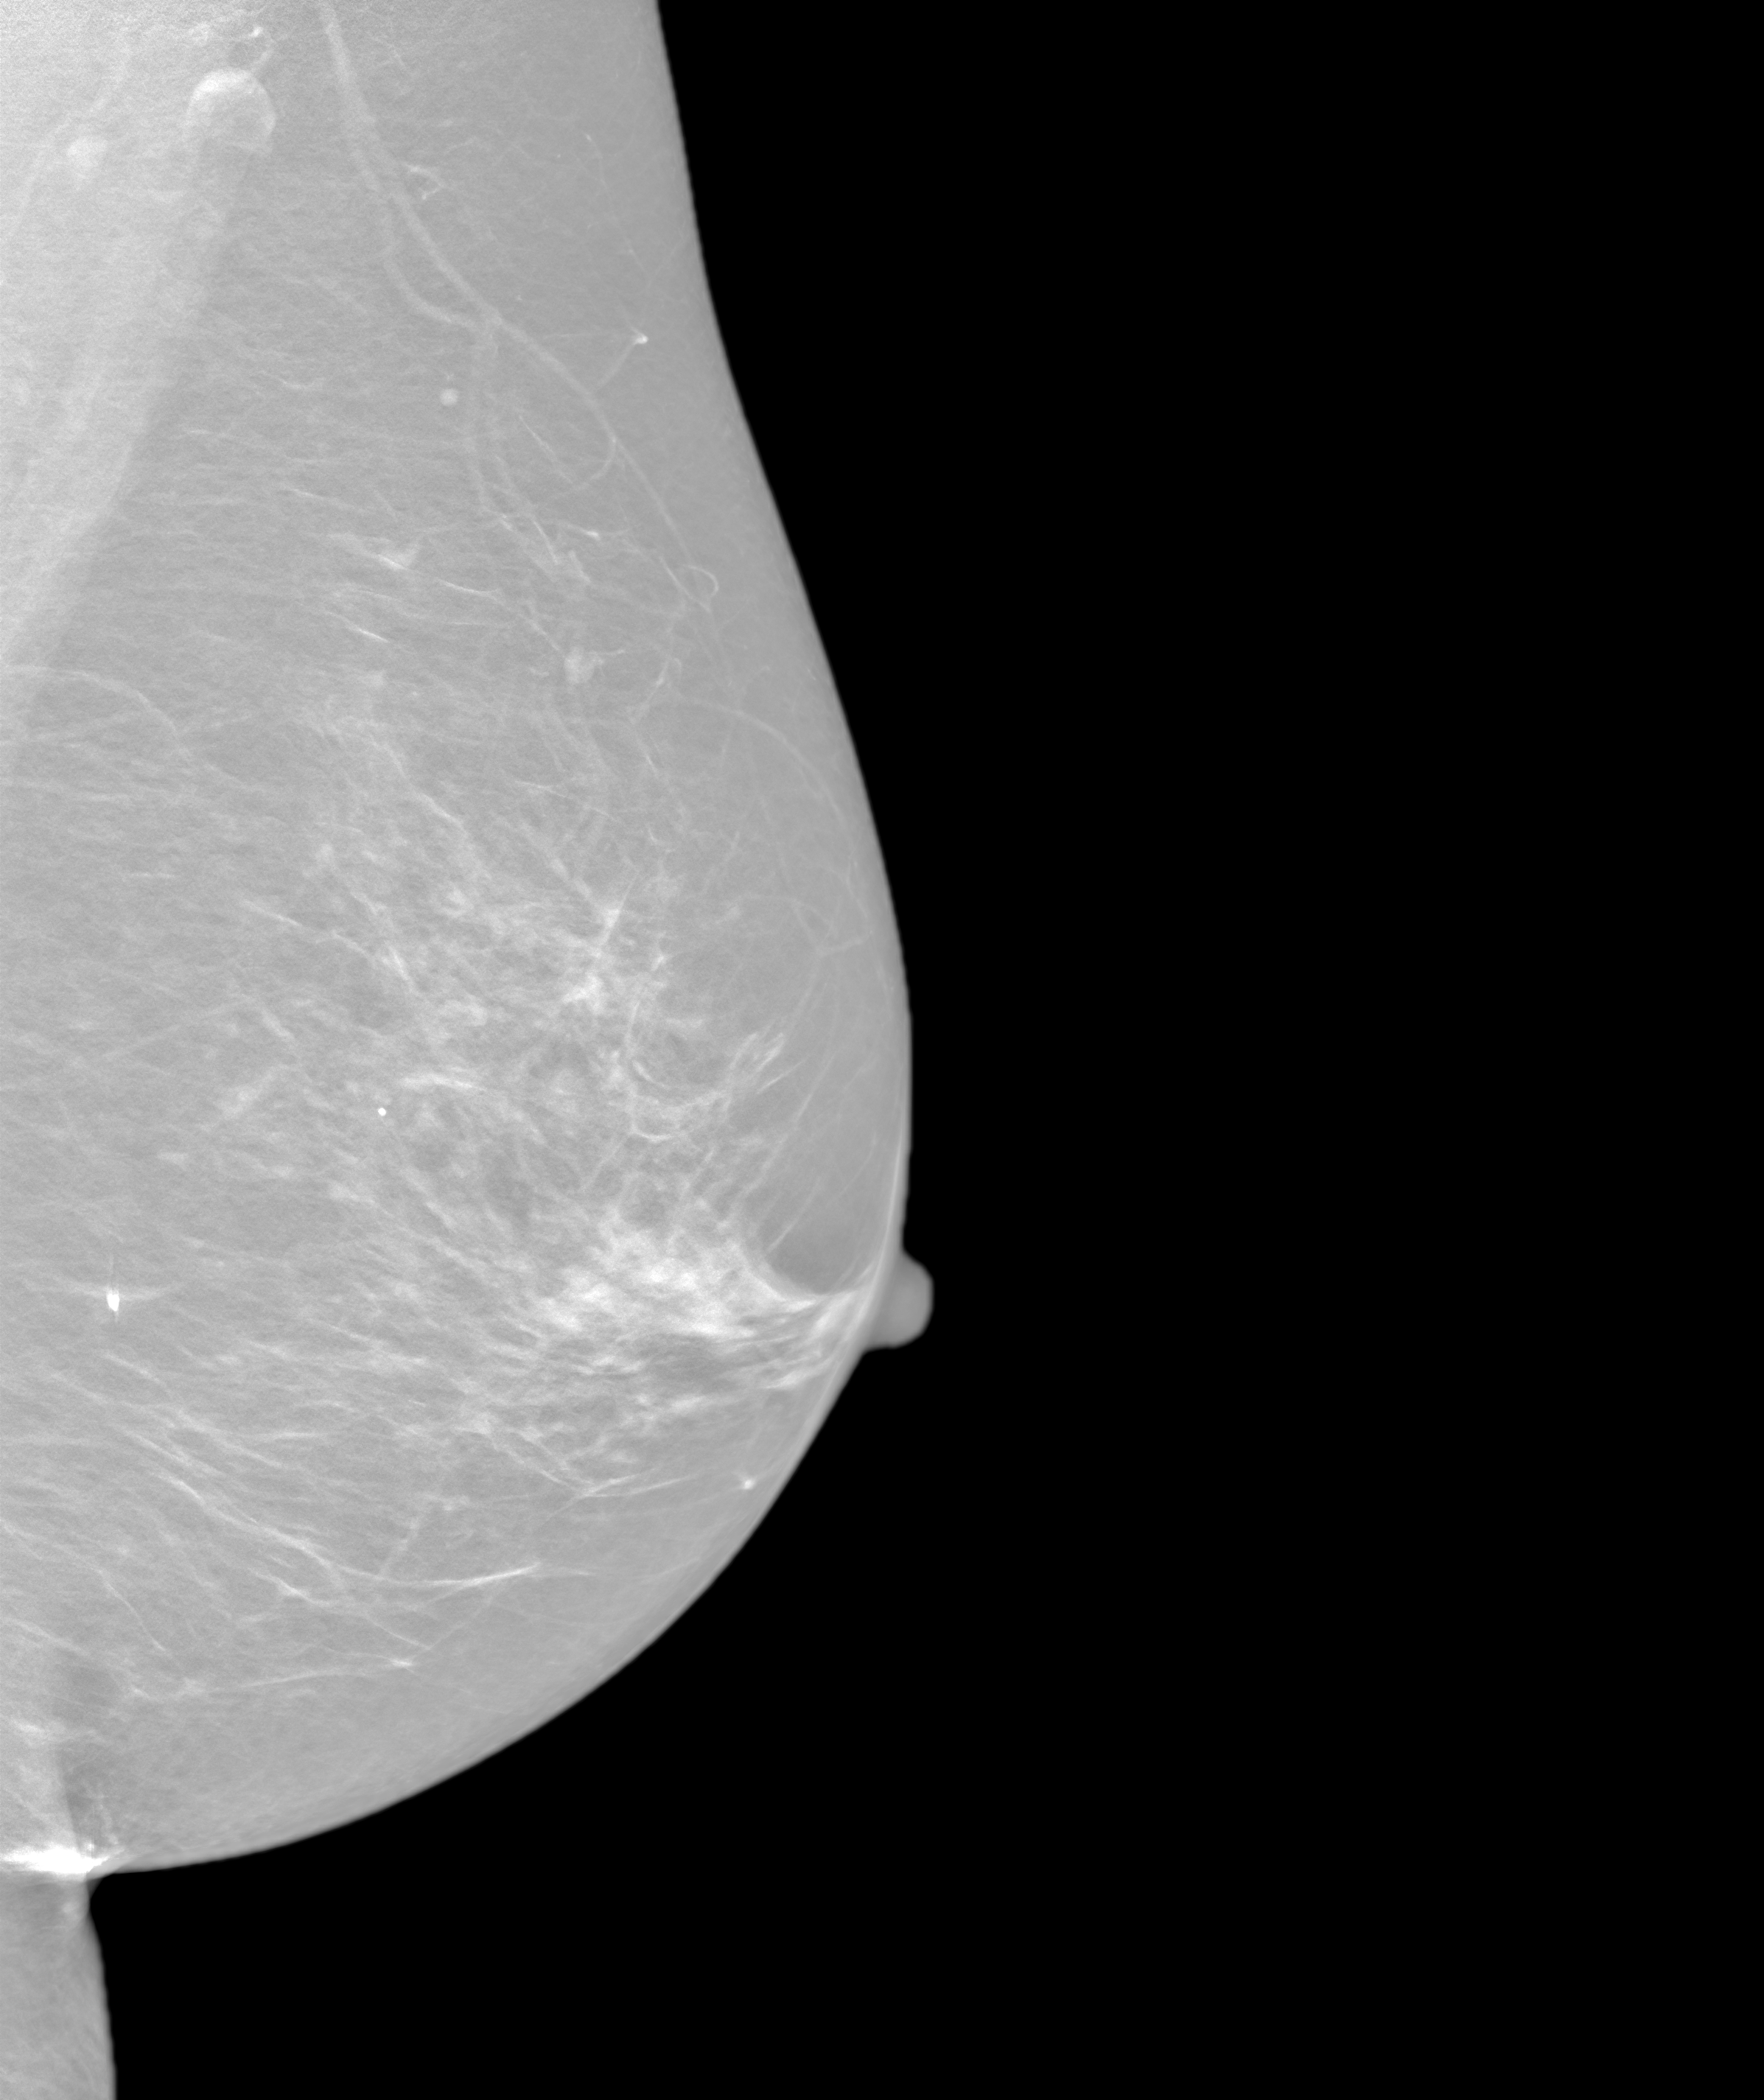
Annual screening mammography examination. Female patient, age 54 years.
Image type: synthesized 2-D view from tomosynthesis. Breast: left. Projection: medio-lateral oblique projection.